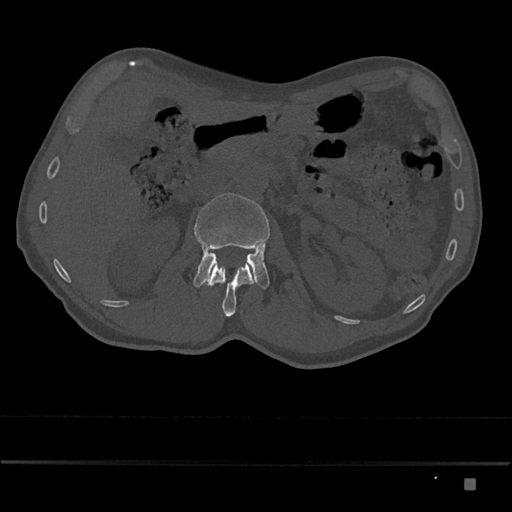
CT including the spine, one axial slice. Position 508 of 797 along the scan axis. 120 kVp. Bone window (W 1800 / L 400 HU). 0.5 mm slice thickness. 512 × 512 image matrix. Male patient, age 72 years. From the clinical record (not read from this slice): primary cancer: prostate.
Structures marked on this image (semi-automatically segmented with operator editing):
- L1 vertebra: bounding box <205,262,256,317> (left, top, right, bottom; pixels)
- L2 vertebra: <193,193,270,289>